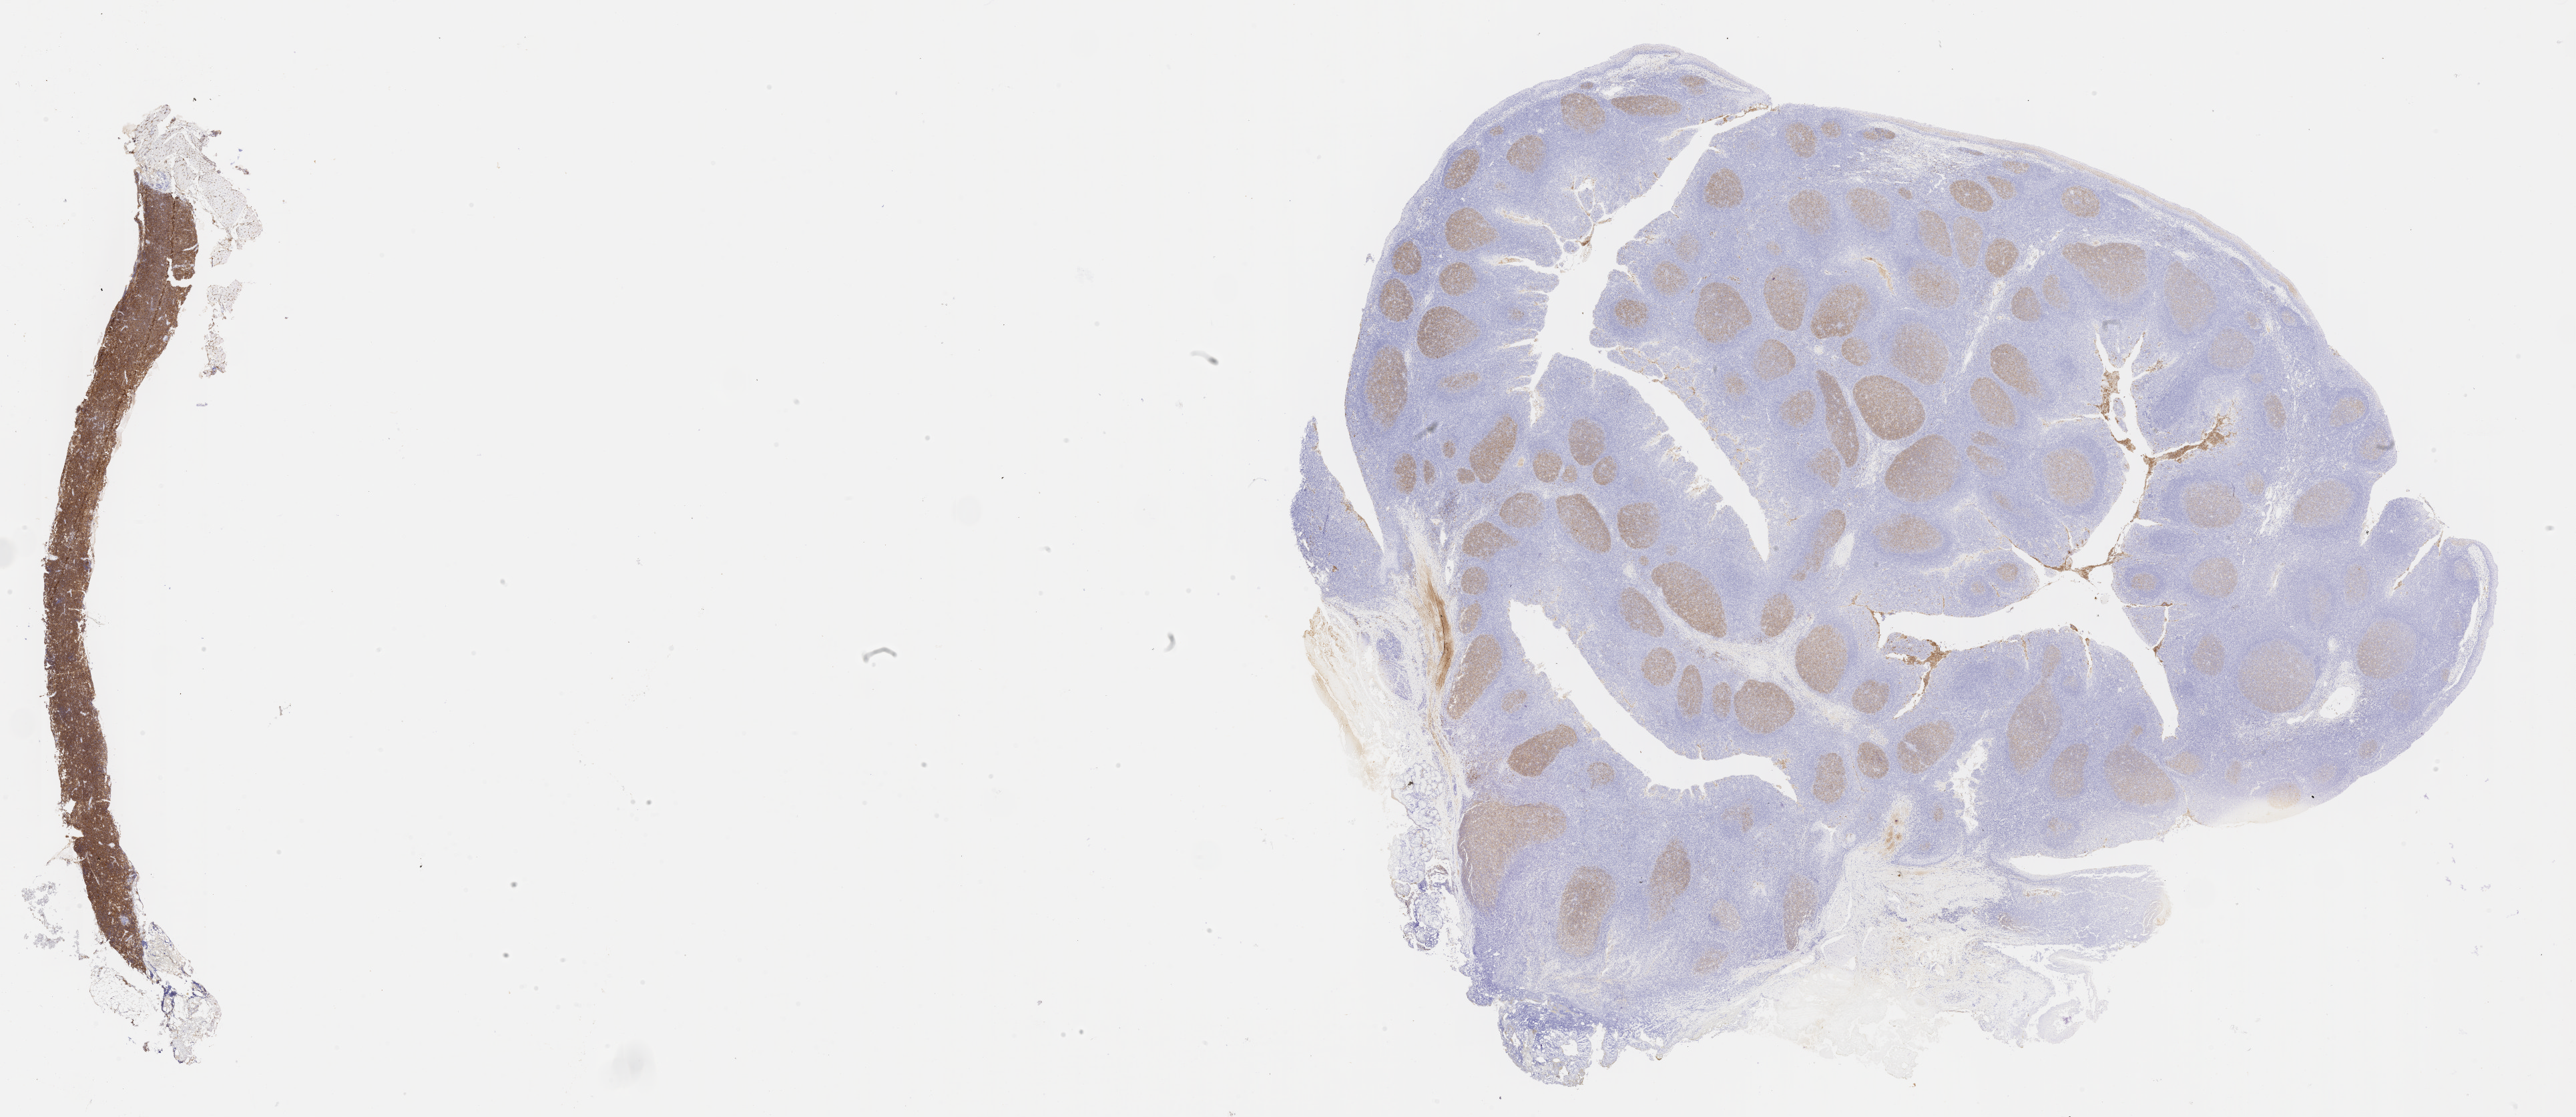
IHC for CD10, whole-slide image, shown as a low-resolution overview of the whole scanned area (about 31.2 x 13.5 mm), tumor tissue, anatomic site: cranium. Female, age 7 years at initial diagnosis.
* histologic diagnosis: Burkitt lymphoma, NOS